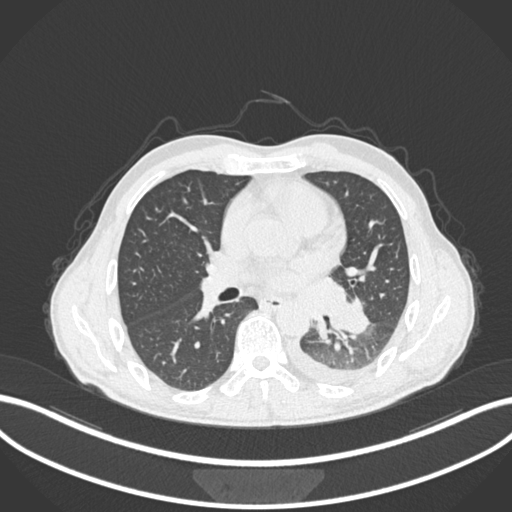
Chest CT, one axial slice. Slice 125 of 222 in the series (ordered by position). Lung window (W 1500 / L -600 HU). 1 mm slice thickness. 512 × 512 image matrix. Patient: male, 47 years. Case-level facts recorded for this patient, not image findings: clinical TNM (as recorded): T3 N1 M1c; histopathological grade: G3.
Annotated regions visible in this slice (rectangle marked by the reading radiologist):
- lung tumour (recorded histology: small cell carcinoma): bounding box <325,290,375,337> (left, top, right, bottom; pixels)